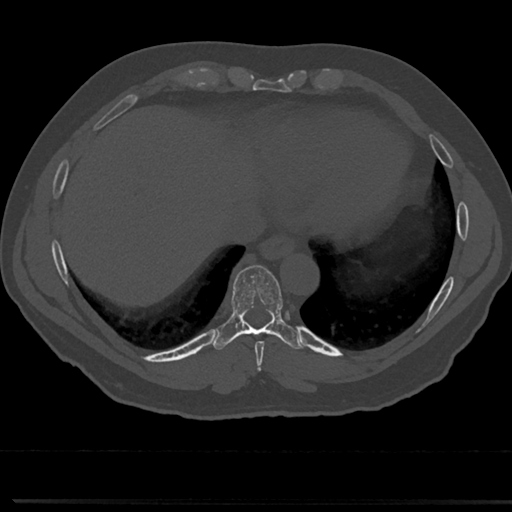
CT including the spine, one axial slice. Slice 314 of 817 in the series (ordered by position). 120 kVp. Bone window (W 1800 / L 400 HU). 0.5 mm slice thickness. 512 × 512 image matrix, field of view 355 × 355 mm. Patient: male, 61 years. Case-level facts recorded for this patient, not image findings: primary cancer: prostate.
Structures marked on this image (semi-automatically segmented with operator editing):
- T7 vertebra: bounding box [x1, y1, x2, y2] px = [258, 365, 265, 375]
- T8 vertebra: [228, 267, 294, 351]
- T9 vertebra: [236, 324, 280, 327]